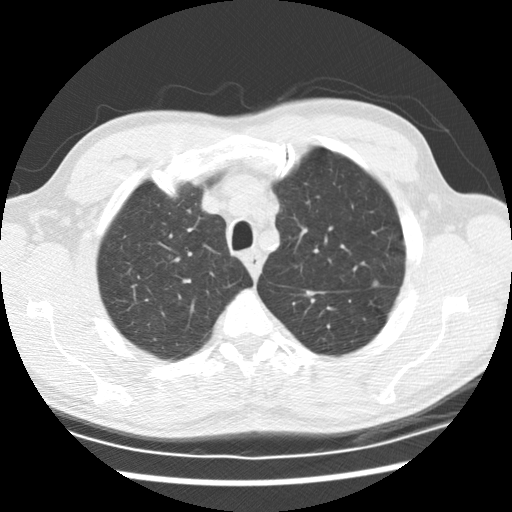
Low-dose screening chest CT, one axial slice. Position 167 of 208 along the scan axis. Reconstruction kernel STANDARD. Lung window (W 1500 / L -600 HU). 2.5 mm slice thickness. 512 × 512 image matrix, field of view 340 × 340 mm.
Outlined on this slice (expert manual segmentation):
- lesion 3 (tumor, upper lobe of left lung): bounding box <372,280,379,287> (left, top, right, bottom; pixels)